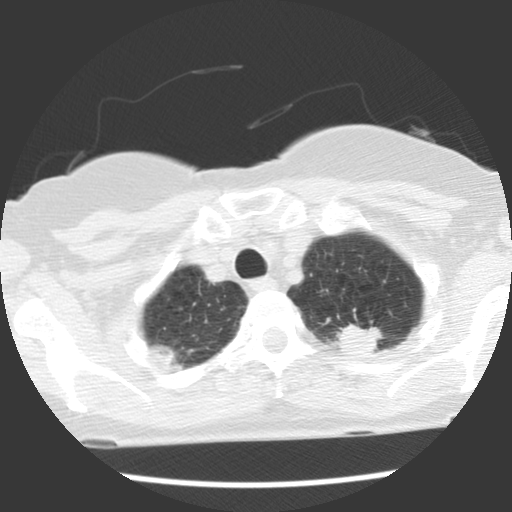
Low-dose screening chest CT, axial slice. Baseline screening round. Lung window (W 1500 / L -600 HU). 2.5 mm slice thickness. Standard (soft-tissue) reconstruction kernel (STANDARD). 140 kVp. Slice 102 of 120 in the series. 512 × 512 image matrix, field of view 300 × 300 mm. Female participant, aged 66 years at enrolment. Former smoker at enrolment.
Expert reader's lesion annotation, box from (x=317, y=304) to (x=386, y=363) px. Screening reader's record for this exam (one nodule recorded; not confirmed to be the boxed lesion): non-calcified nodule or mass ≥4 mm, left upper lobe, 22 × 17 mm, spiculated (stellate) margins, soft tissue attenuation. Official screen result: positive, change unspecified: nodule(s) >= 4 mm or enlarging nodule(s), mass(es), or other non-specific abnormalities suspicious for lung cancer. Later outcome: lung cancer diagnosed 50 days after this screen — adenocarcinoma, NOS, left upper lobe, poorly differentiated (G3), stage IB (AJCC 6th edition), 40 mm at pathology.